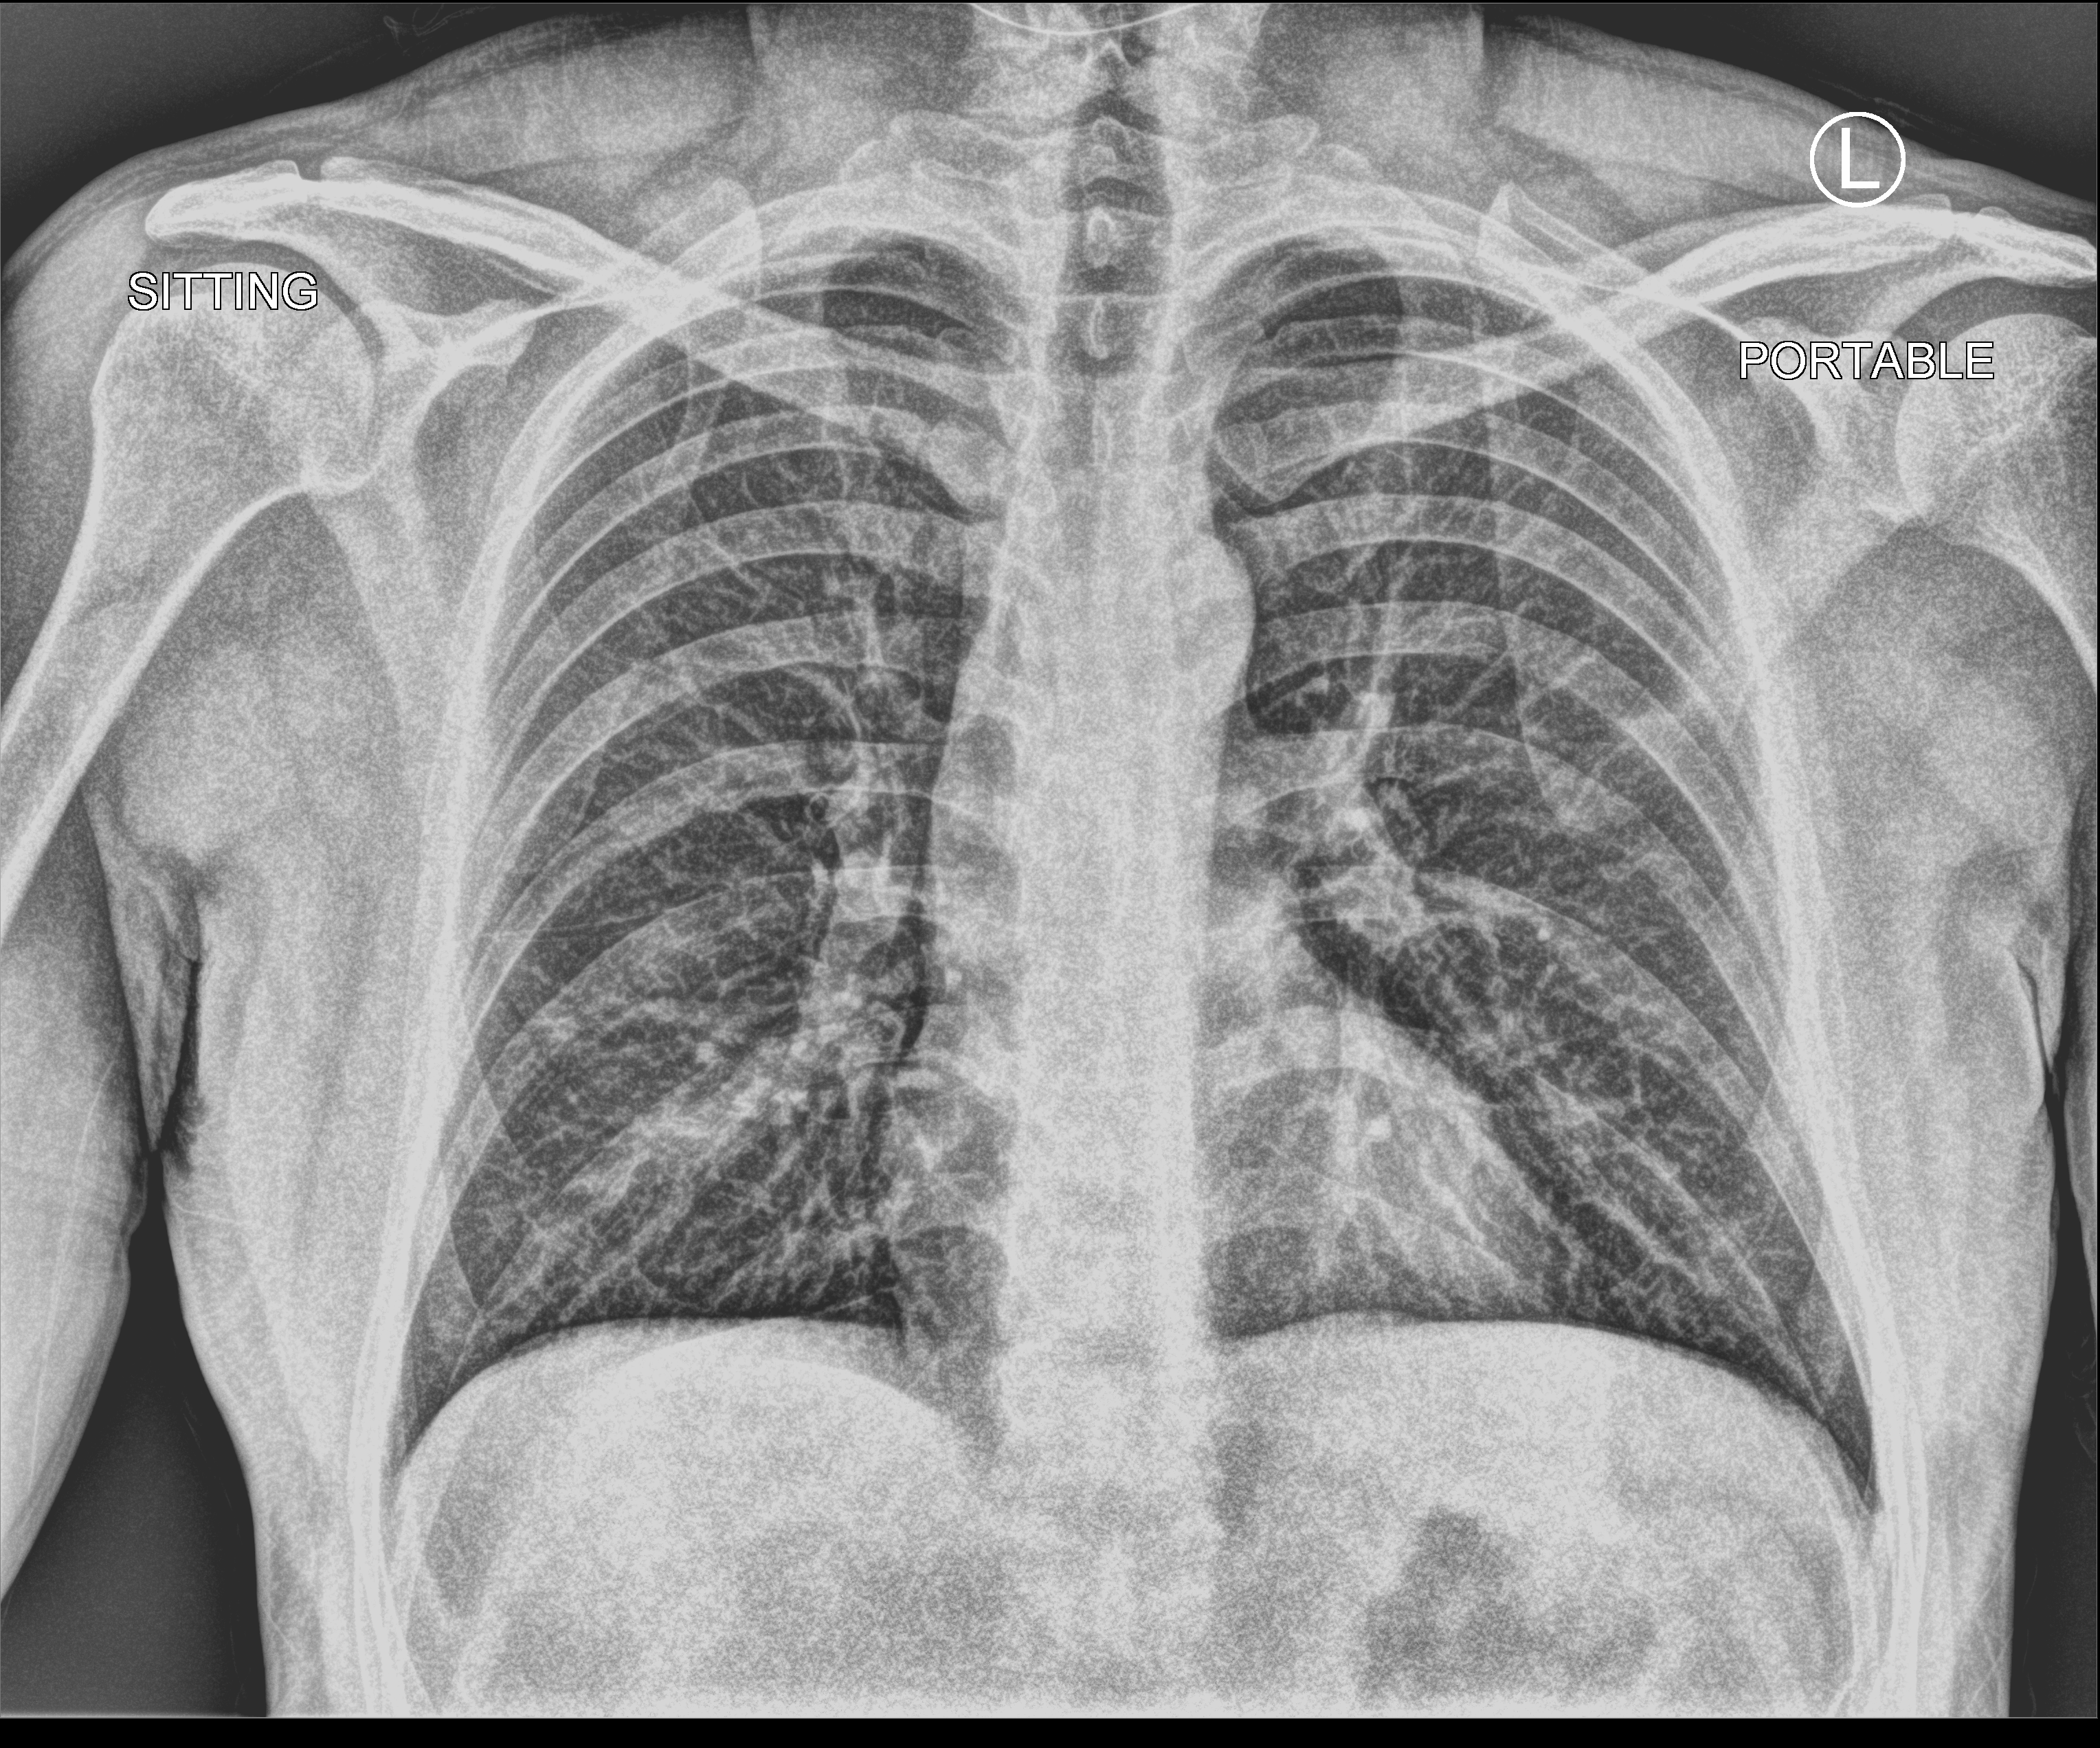
Chest X-ray (portable); anteroposterior (AP) projection. Patient hospitalised with COVID-19; male, aged 18–59 years.
From the hospital-stay record, not from the radiograph (when in the stay this image was taken is not recorded): other chronic lung disease (admission record): no; admitted to intensive care during this hospital stay: no; mechanically ventilated during this hospital stay: no.